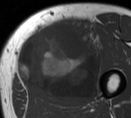
MRI of an extremity soft-tissue mass, one axial slice; position 29 of 55 along the scan axis; MR volume resampled by the dataset authors to the PET/CT grid (not the native acquisition matrix); 3.27 mm slice thickness; 131 × 118 image matrix. Male patient. Case-level facts recorded for this patient, not image findings: histological type: pleiomorphic liposarcoma; grade: high; site of the primary tumour: left thigh.
Structures marked on this image (expert contour drawn on MRI and transferred to this co-registered scan by the dataset authors):
- gross tumour volume including surrounding oedema: bounding box [x1, y1, x2, y2] px = [14, 20, 106, 104]
- gross tumour volume (mass): [14, 20, 101, 104]